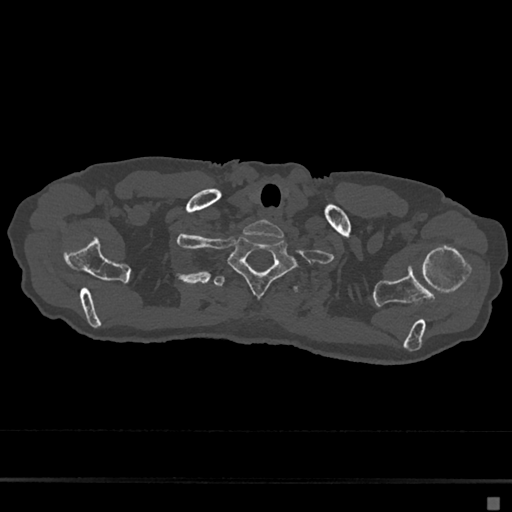
CT including the spine, one axial slice; slice 607 of 797 in the series (ordered by position); reconstruction kernel Br40s/3; bone window (W 1800 / L 400 HU); 512 × 512 image matrix, field of view 360 × 360 mm. Female patient, age 68 years. Case-level facts recorded for this patient, not image findings: primary cancer: renal.
Structures marked on this image (semi-automatically segmented with operator editing):
- T1 vertebra: box from (x=228, y=236) to (x=296, y=297) px
- T2 vertebra: (x=213, y=276)–(x=302, y=293)